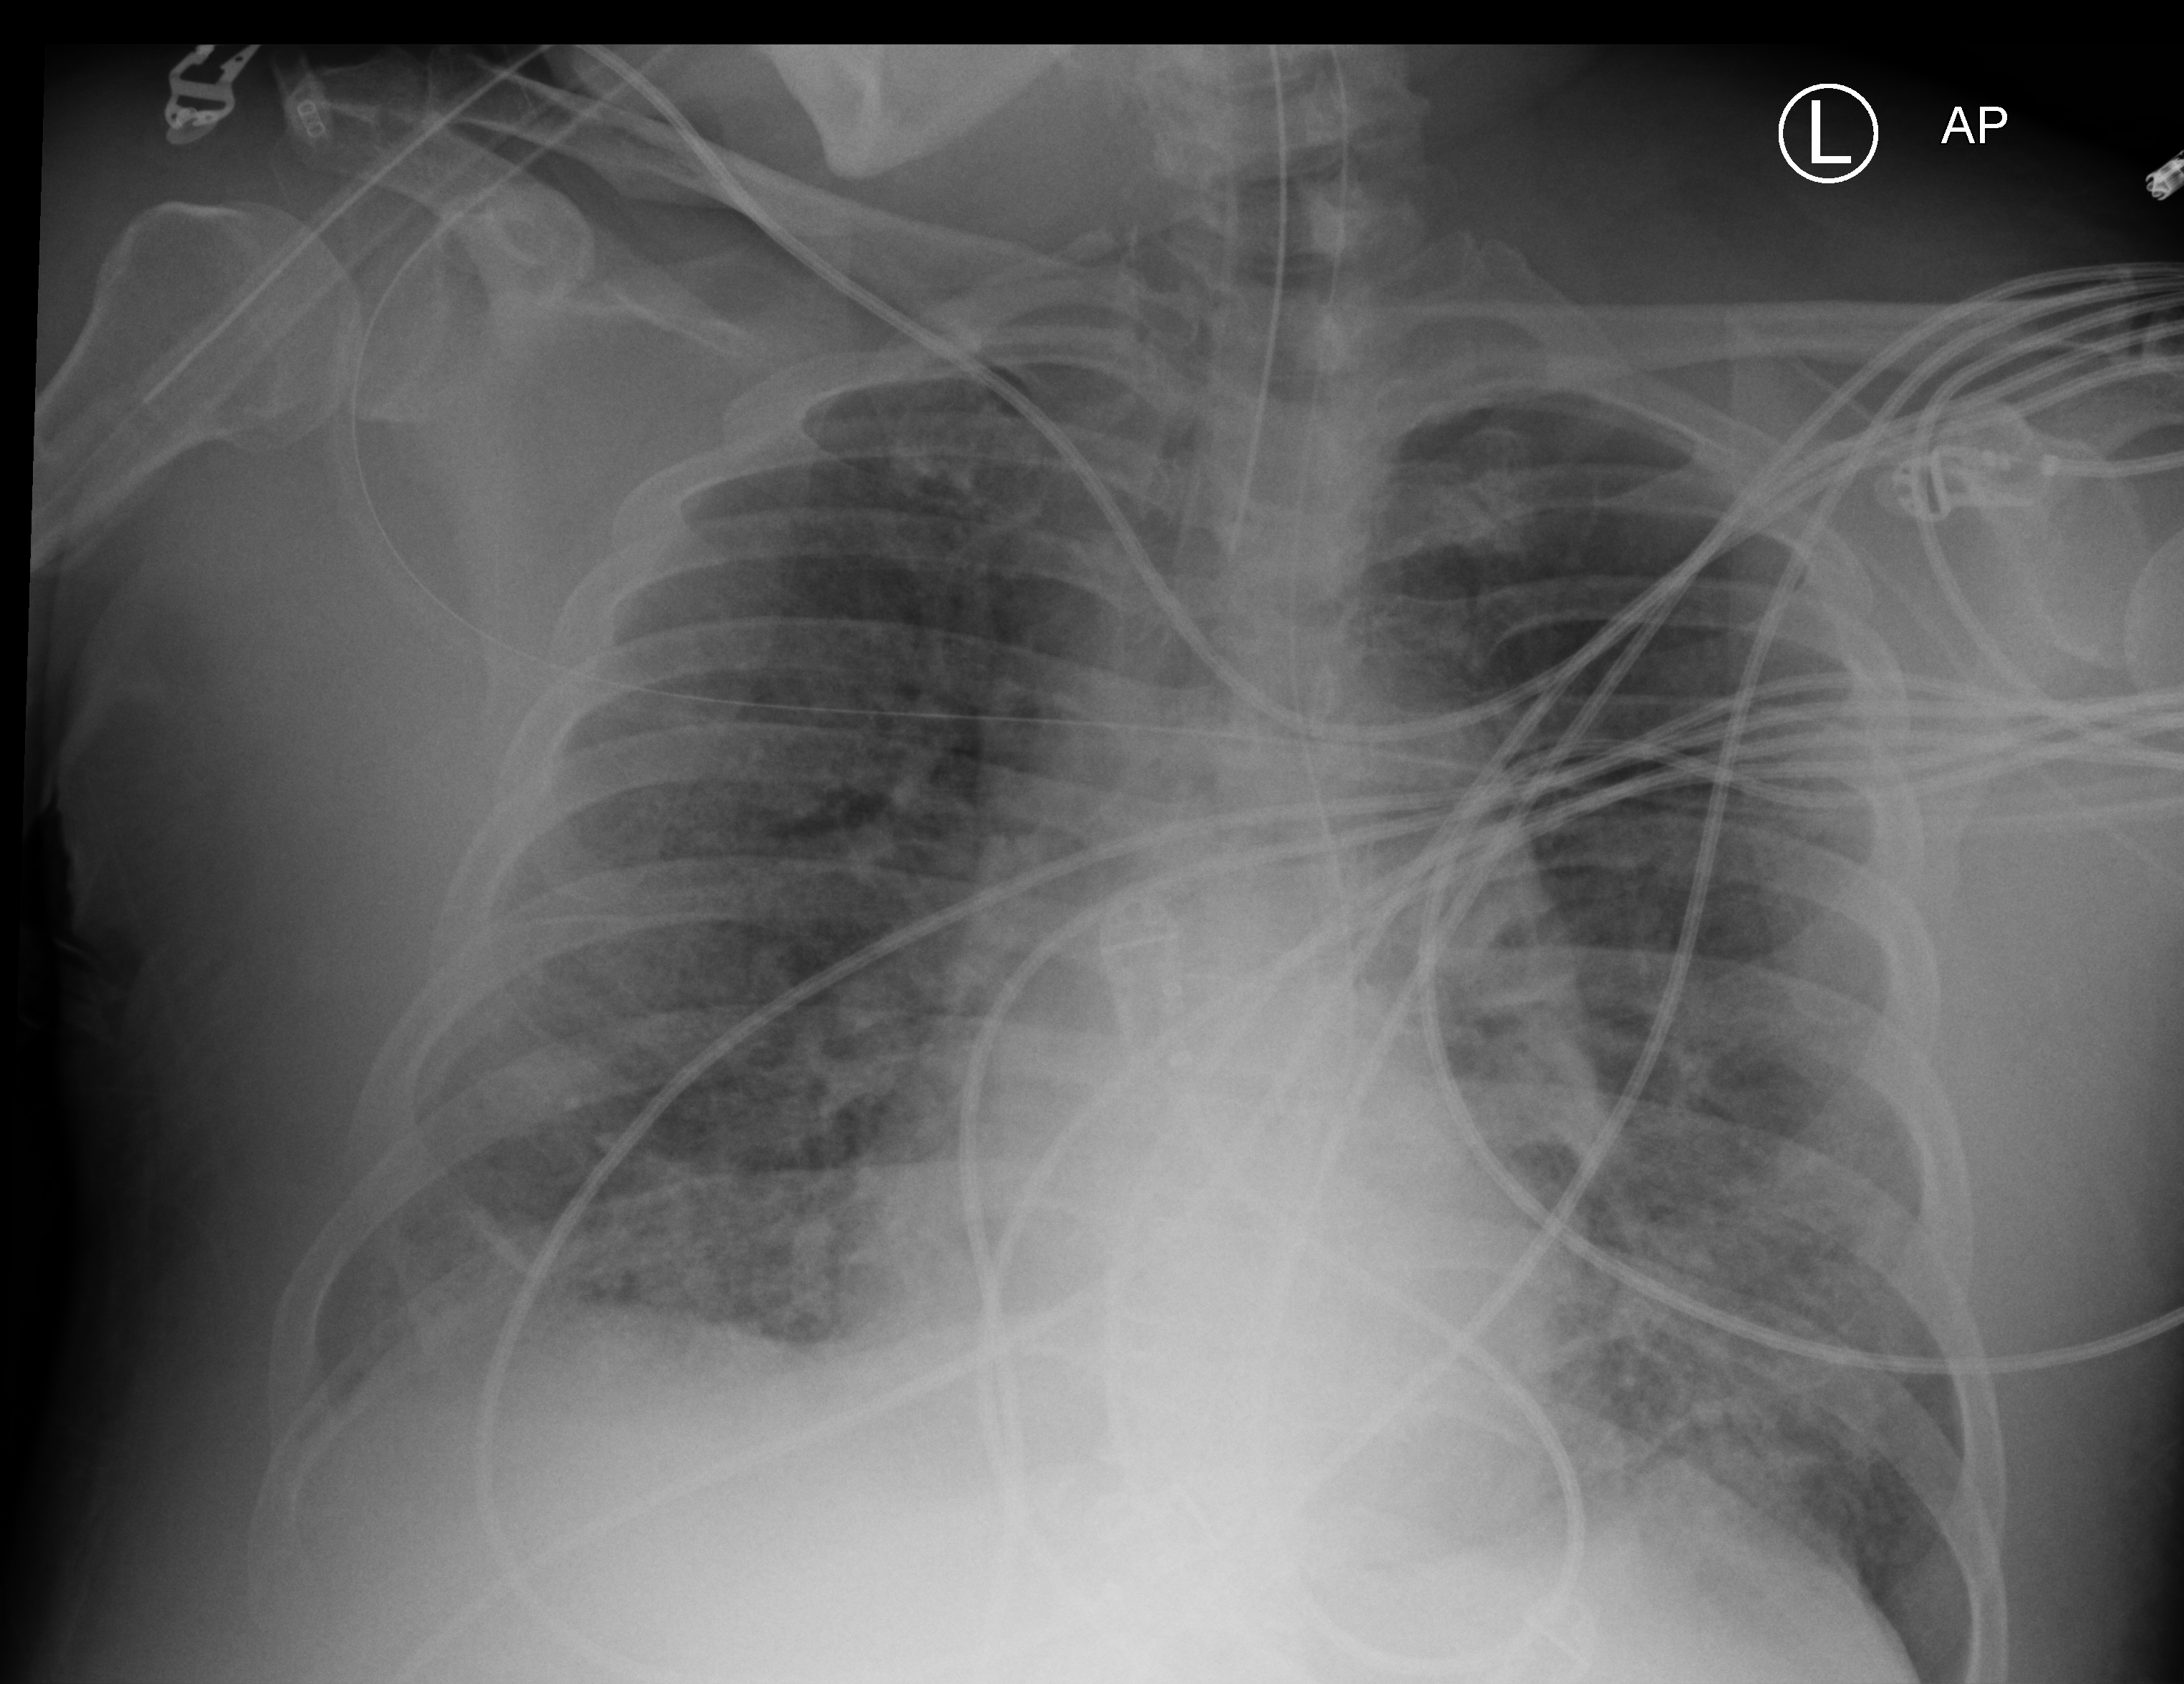
Chest X-ray (portable); anteroposterior (AP) projection. Male patient hospitalised with COVID-19, age 60–74 years.
From the hospital-stay record, not from the radiograph (when in the stay this image was taken is not recorded): admitted to intensive care during this hospital stay: yes.